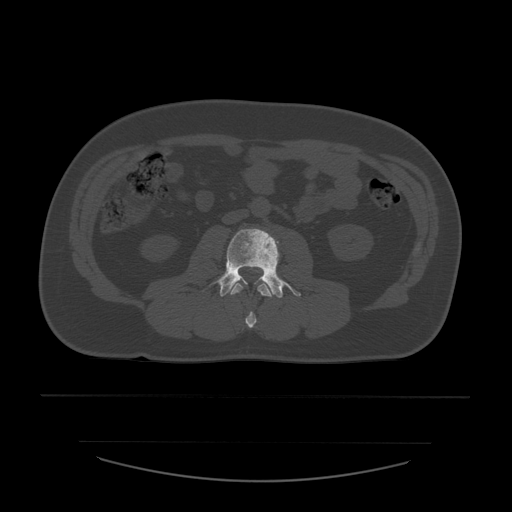
CT including the spine, one axial slice. Position 181 of 532 along the scan axis. 120 kVp. Bone window (W 1800 / L 400 HU). 1.25 mm slice thickness. 512 × 512 image matrix. Patient age 44 years. Case-level facts recorded for this patient, not image findings: primary cancer: soft tissue sarcoma.
Outlined on this slice (semi-automatic segmentation, software-assisted and operator-edited):
- L2 vertebra: box from (x=231, y=283) to (x=273, y=329) px
- L3 vertebra: (x=218, y=229)–(x=301, y=299)